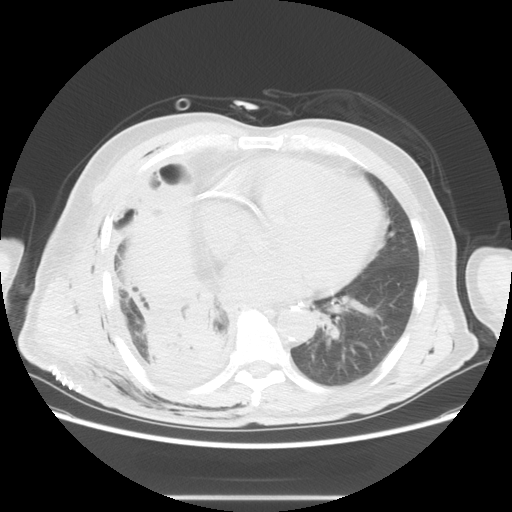
Chest CT, one axial slice. Slice 27 of 59 in the series (ordered by position). Reconstruction kernel STANDARD. Lung window (W 1500 / L -600 HU). 512 × 512 image matrix. Patient: male, 69 years. Case-level facts recorded for this patient, not image findings: clinical TNM (as recorded): T3 N0 M0.
Annotated regions visible in this slice (rectangle marked by the reading radiologist):
- lung tumour (recorded histology: squamous cell carcinoma): bounding box [x1, y1, x2, y2] px = [134, 289, 236, 388]